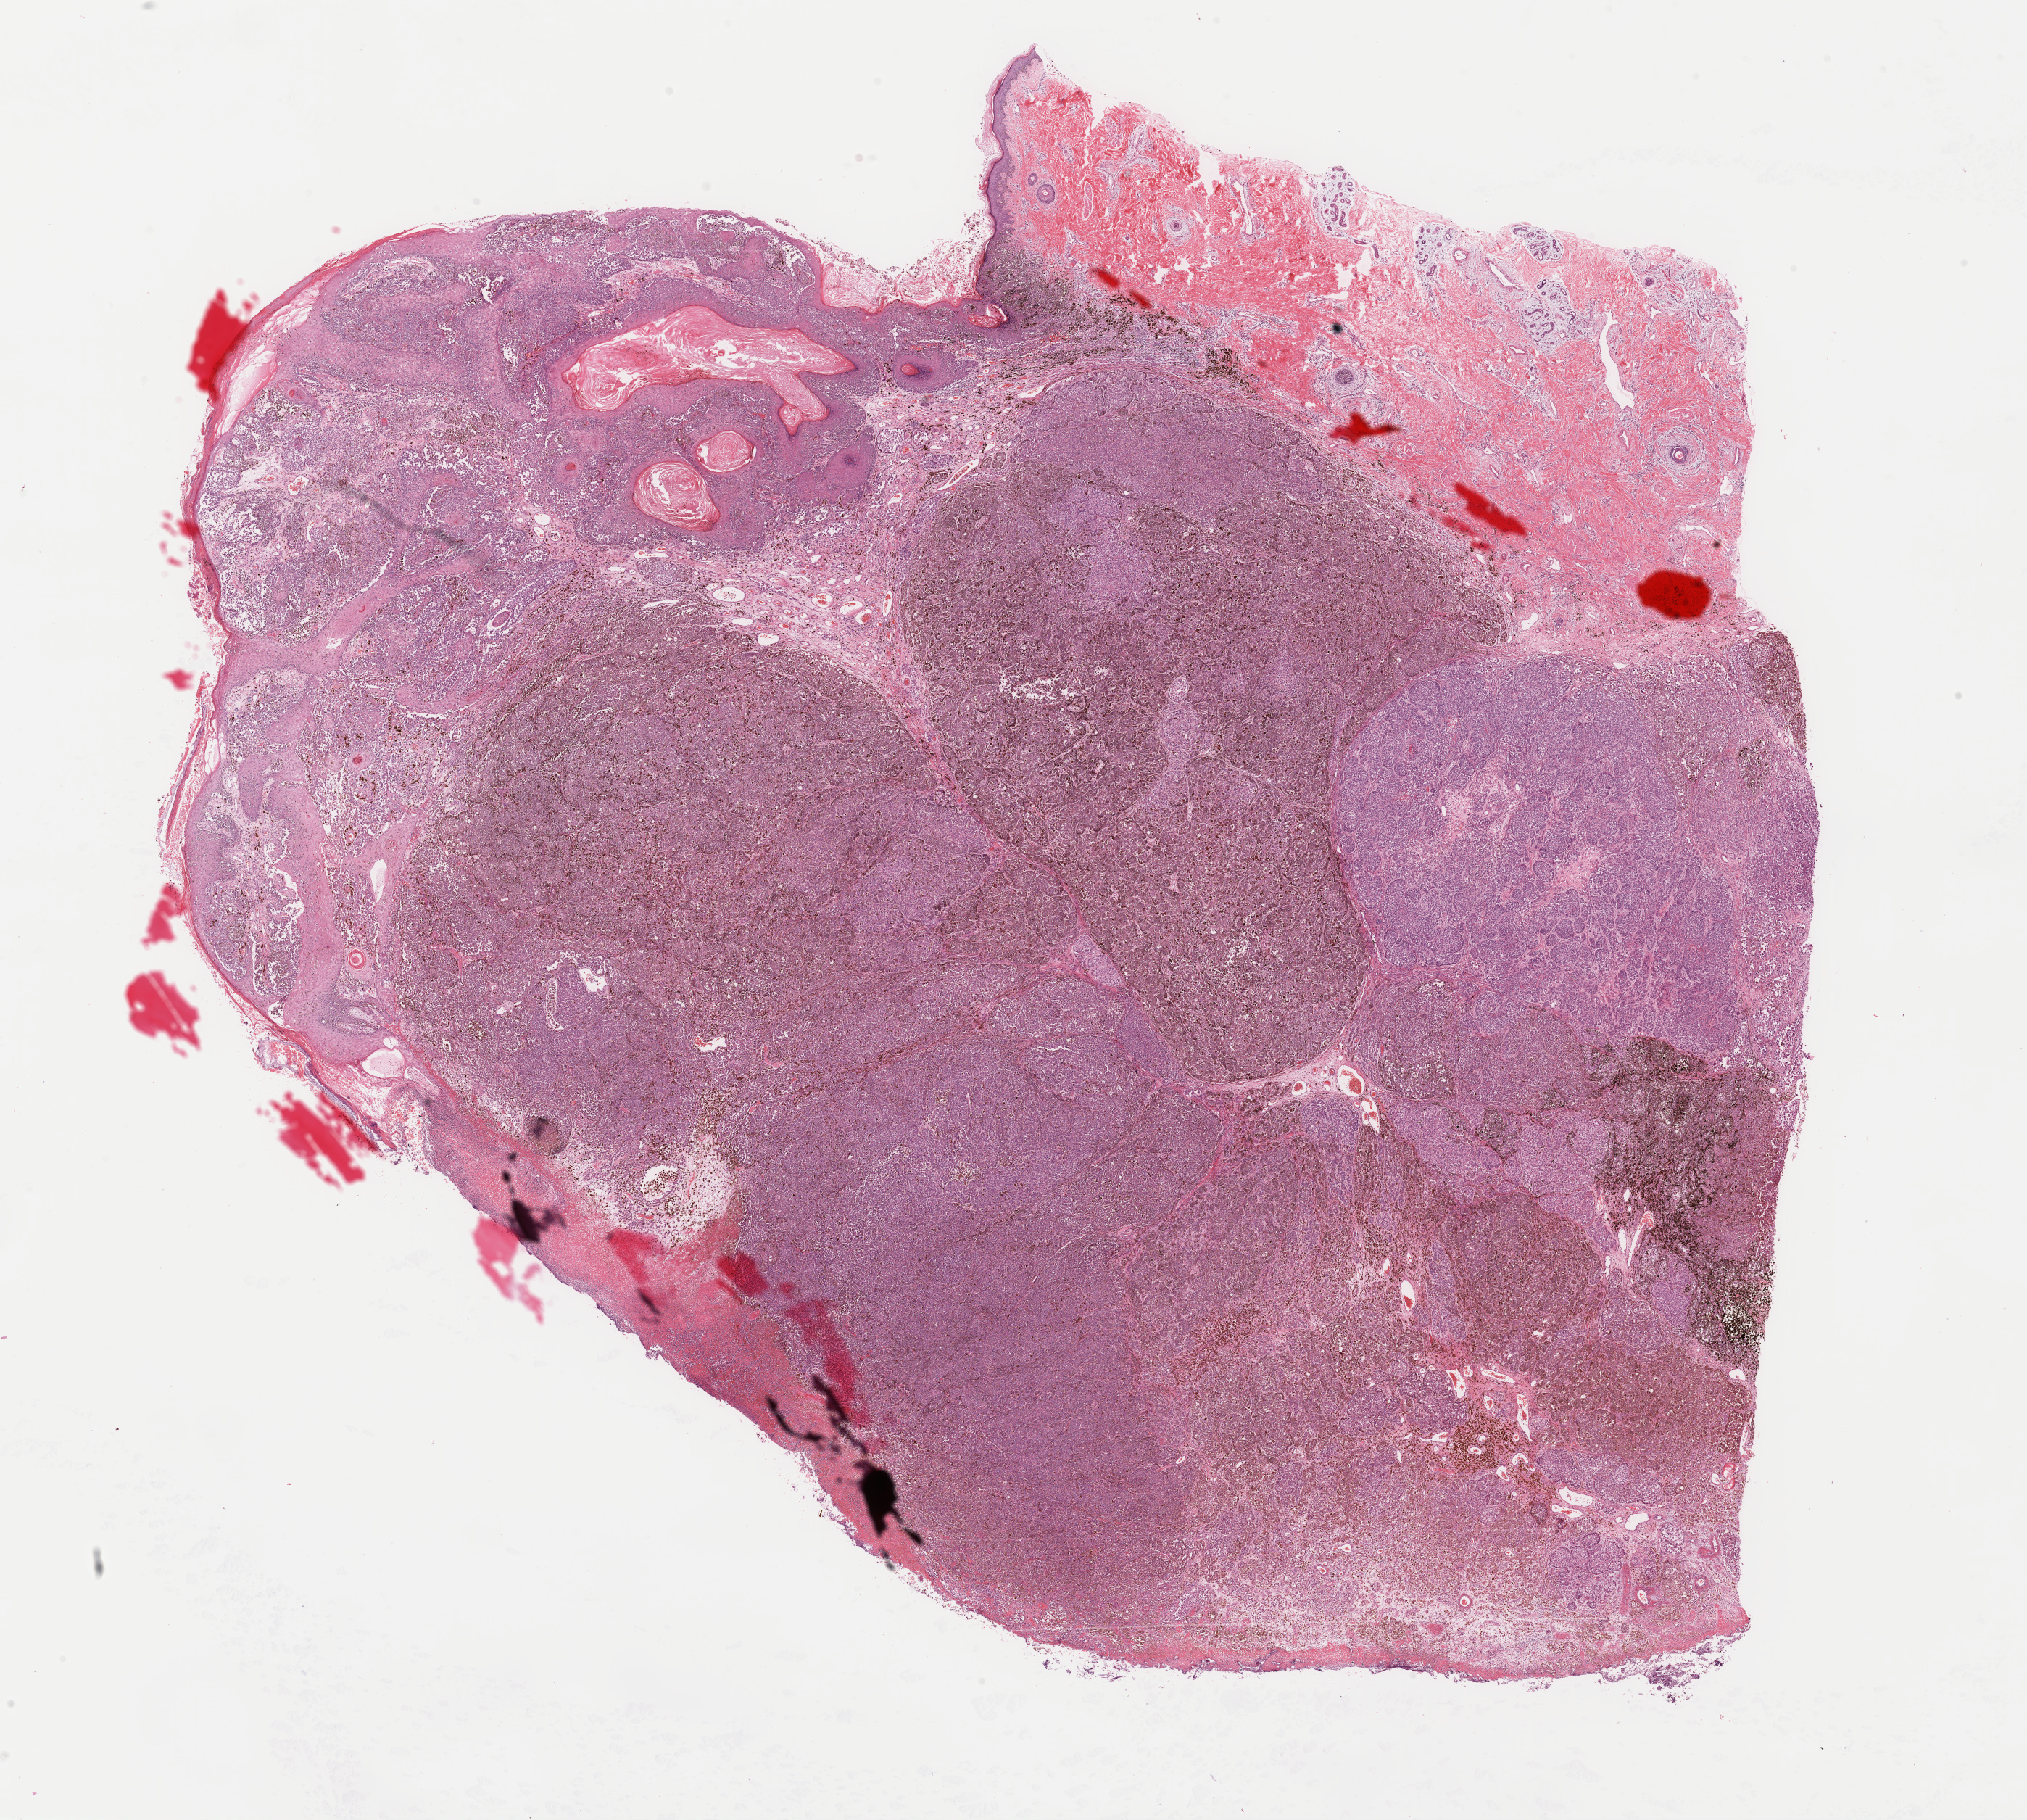
Digitized H&E-stained tissue section (whole slide), shown as a low-resolution overview of the whole scanned area (about 22.1 x 19.8 mm, from a 40x scan). Formalin-fixed paraffin-embedded (FFPE) diagnostic section. Sample: primary tumour, skin. Female patient; age at initial diagnosis 42 years.
Pathologic diagnosis: Malignant melanoma, NOS. AJCC pathologic stage: IIIB.